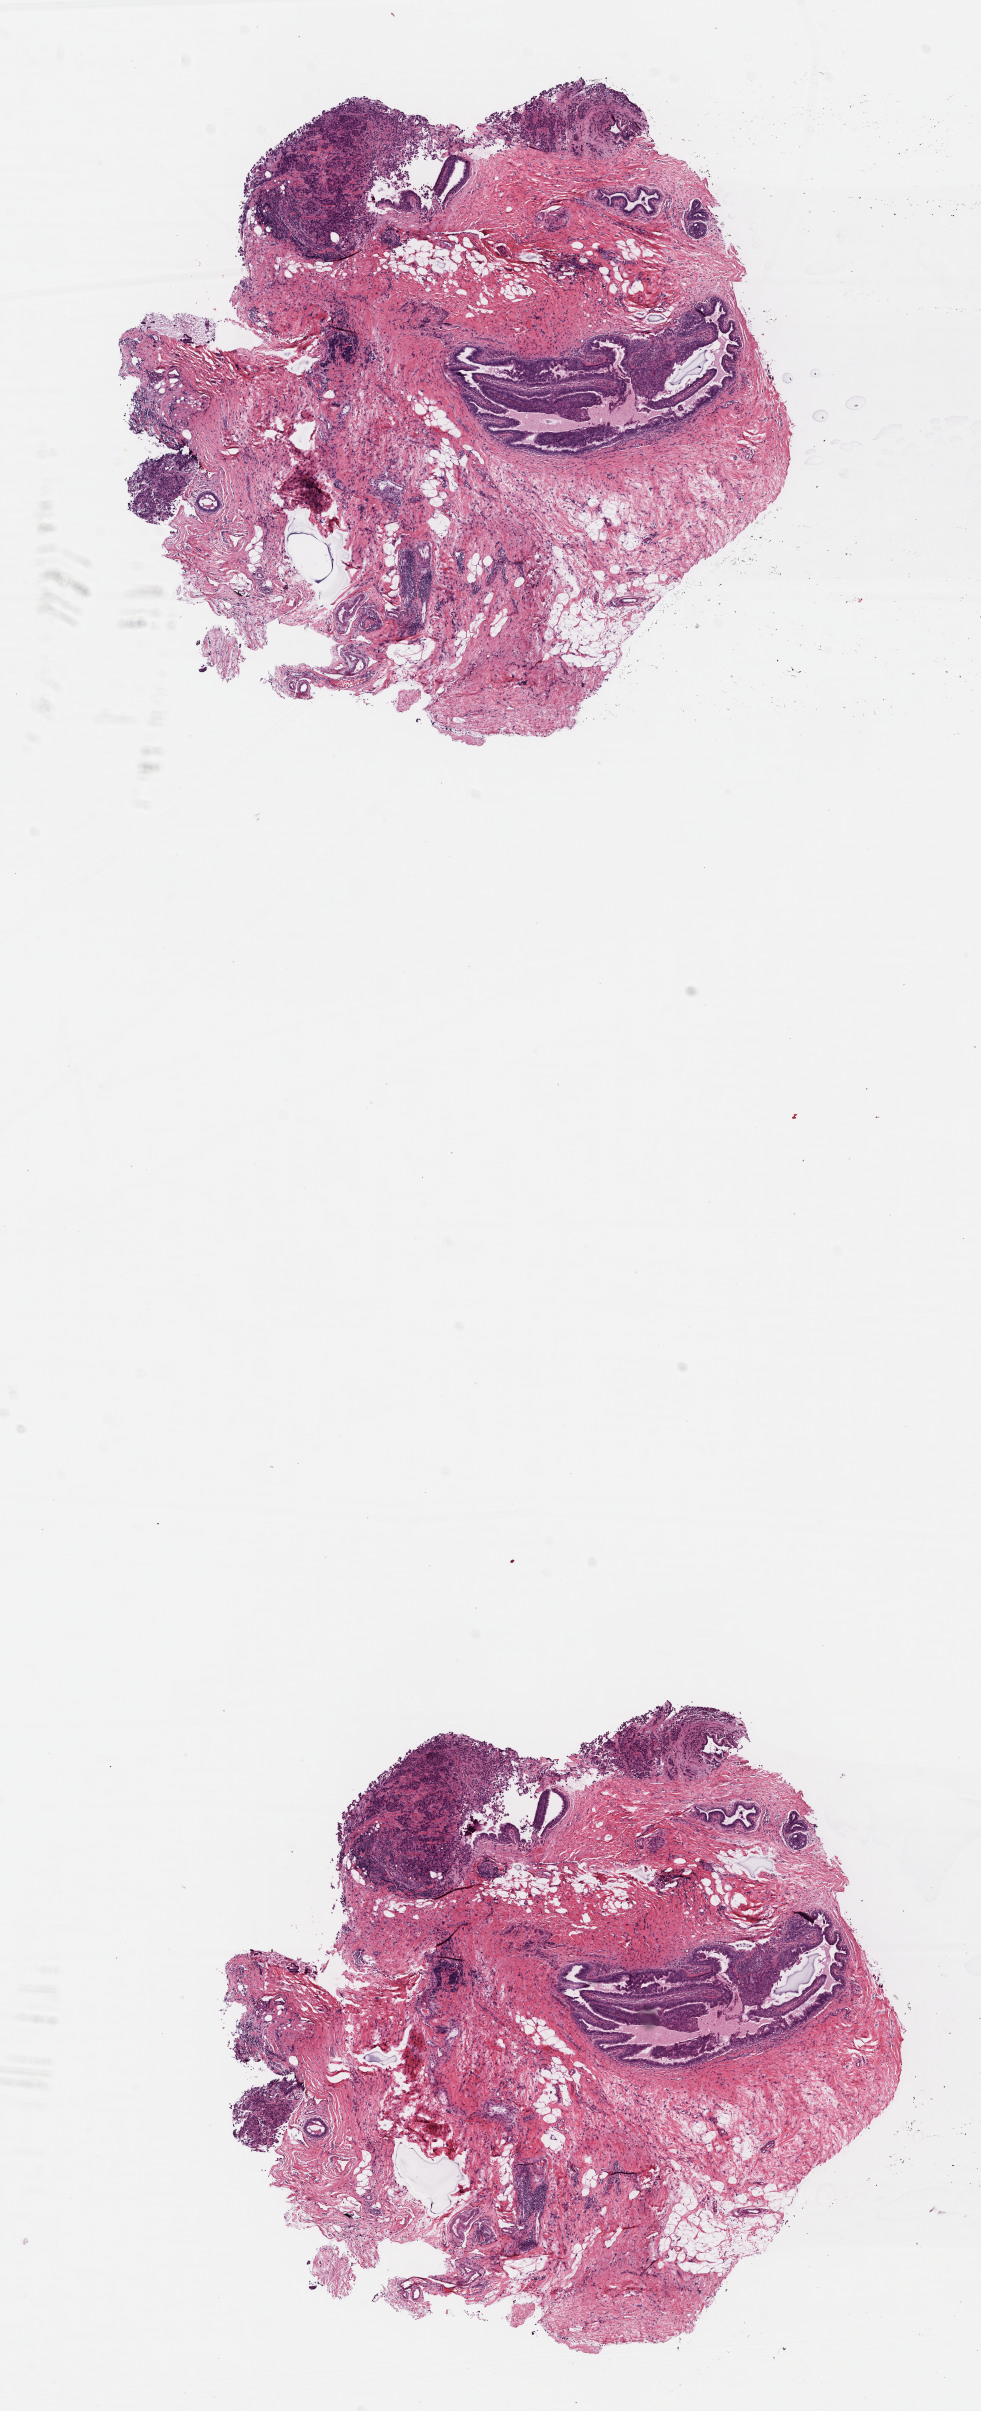
H&E-stained whole-slide image, a low-resolution overview of the entire scanned area, about 7.7 x 19.0 mm (acquisition: 40x scan); formalin-fixed paraffin-embedded (FFPE) diagnostic section; primary tumour sample from the breast. Patient: female, age at initial diagnosis 57 years.
Histologic diagnosis: Infiltrating duct carcinoma, NOS. AJCC pathologic stage: IIA. Laterality: left.